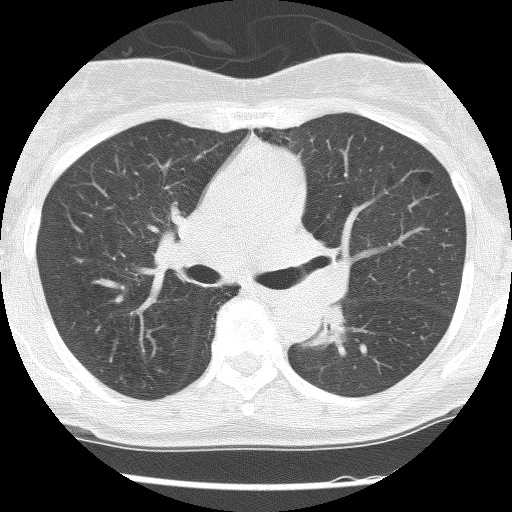
Chest CT (low-dose screening protocol), one axial image, second annual screen, lung window (W 1500 / L -600 HU), 2.5 mm slice thickness, lung (sharp) reconstruction kernel (BONE), 120 kVp, slice 50 of 120 in the series. Female participant, aged 62 years at enrolment. Former smoker at enrolment.
• Lesion marked by an expert reader, bounding box (x1, y1, x2, y2) in pixels: (298, 305, 351, 353).
• Reader record for this screening exam (exam-level; its link to the box is not recorded): non-calcified nodule or mass ≥4 mm, right upper lobe, 30 × 30 mm, poorly defined margins, ground glass attenuation, pre-existing on the prior screen: yes; interval growth: no.
• Note: the box lies in the patient's left hemithorax on this image, whereas the reader's record names the right lung; they may be different findings.
• Official screen result: positive, no significant change: stable abnormalities potentially related to lung cancer, unchanged since the prior screening exam.